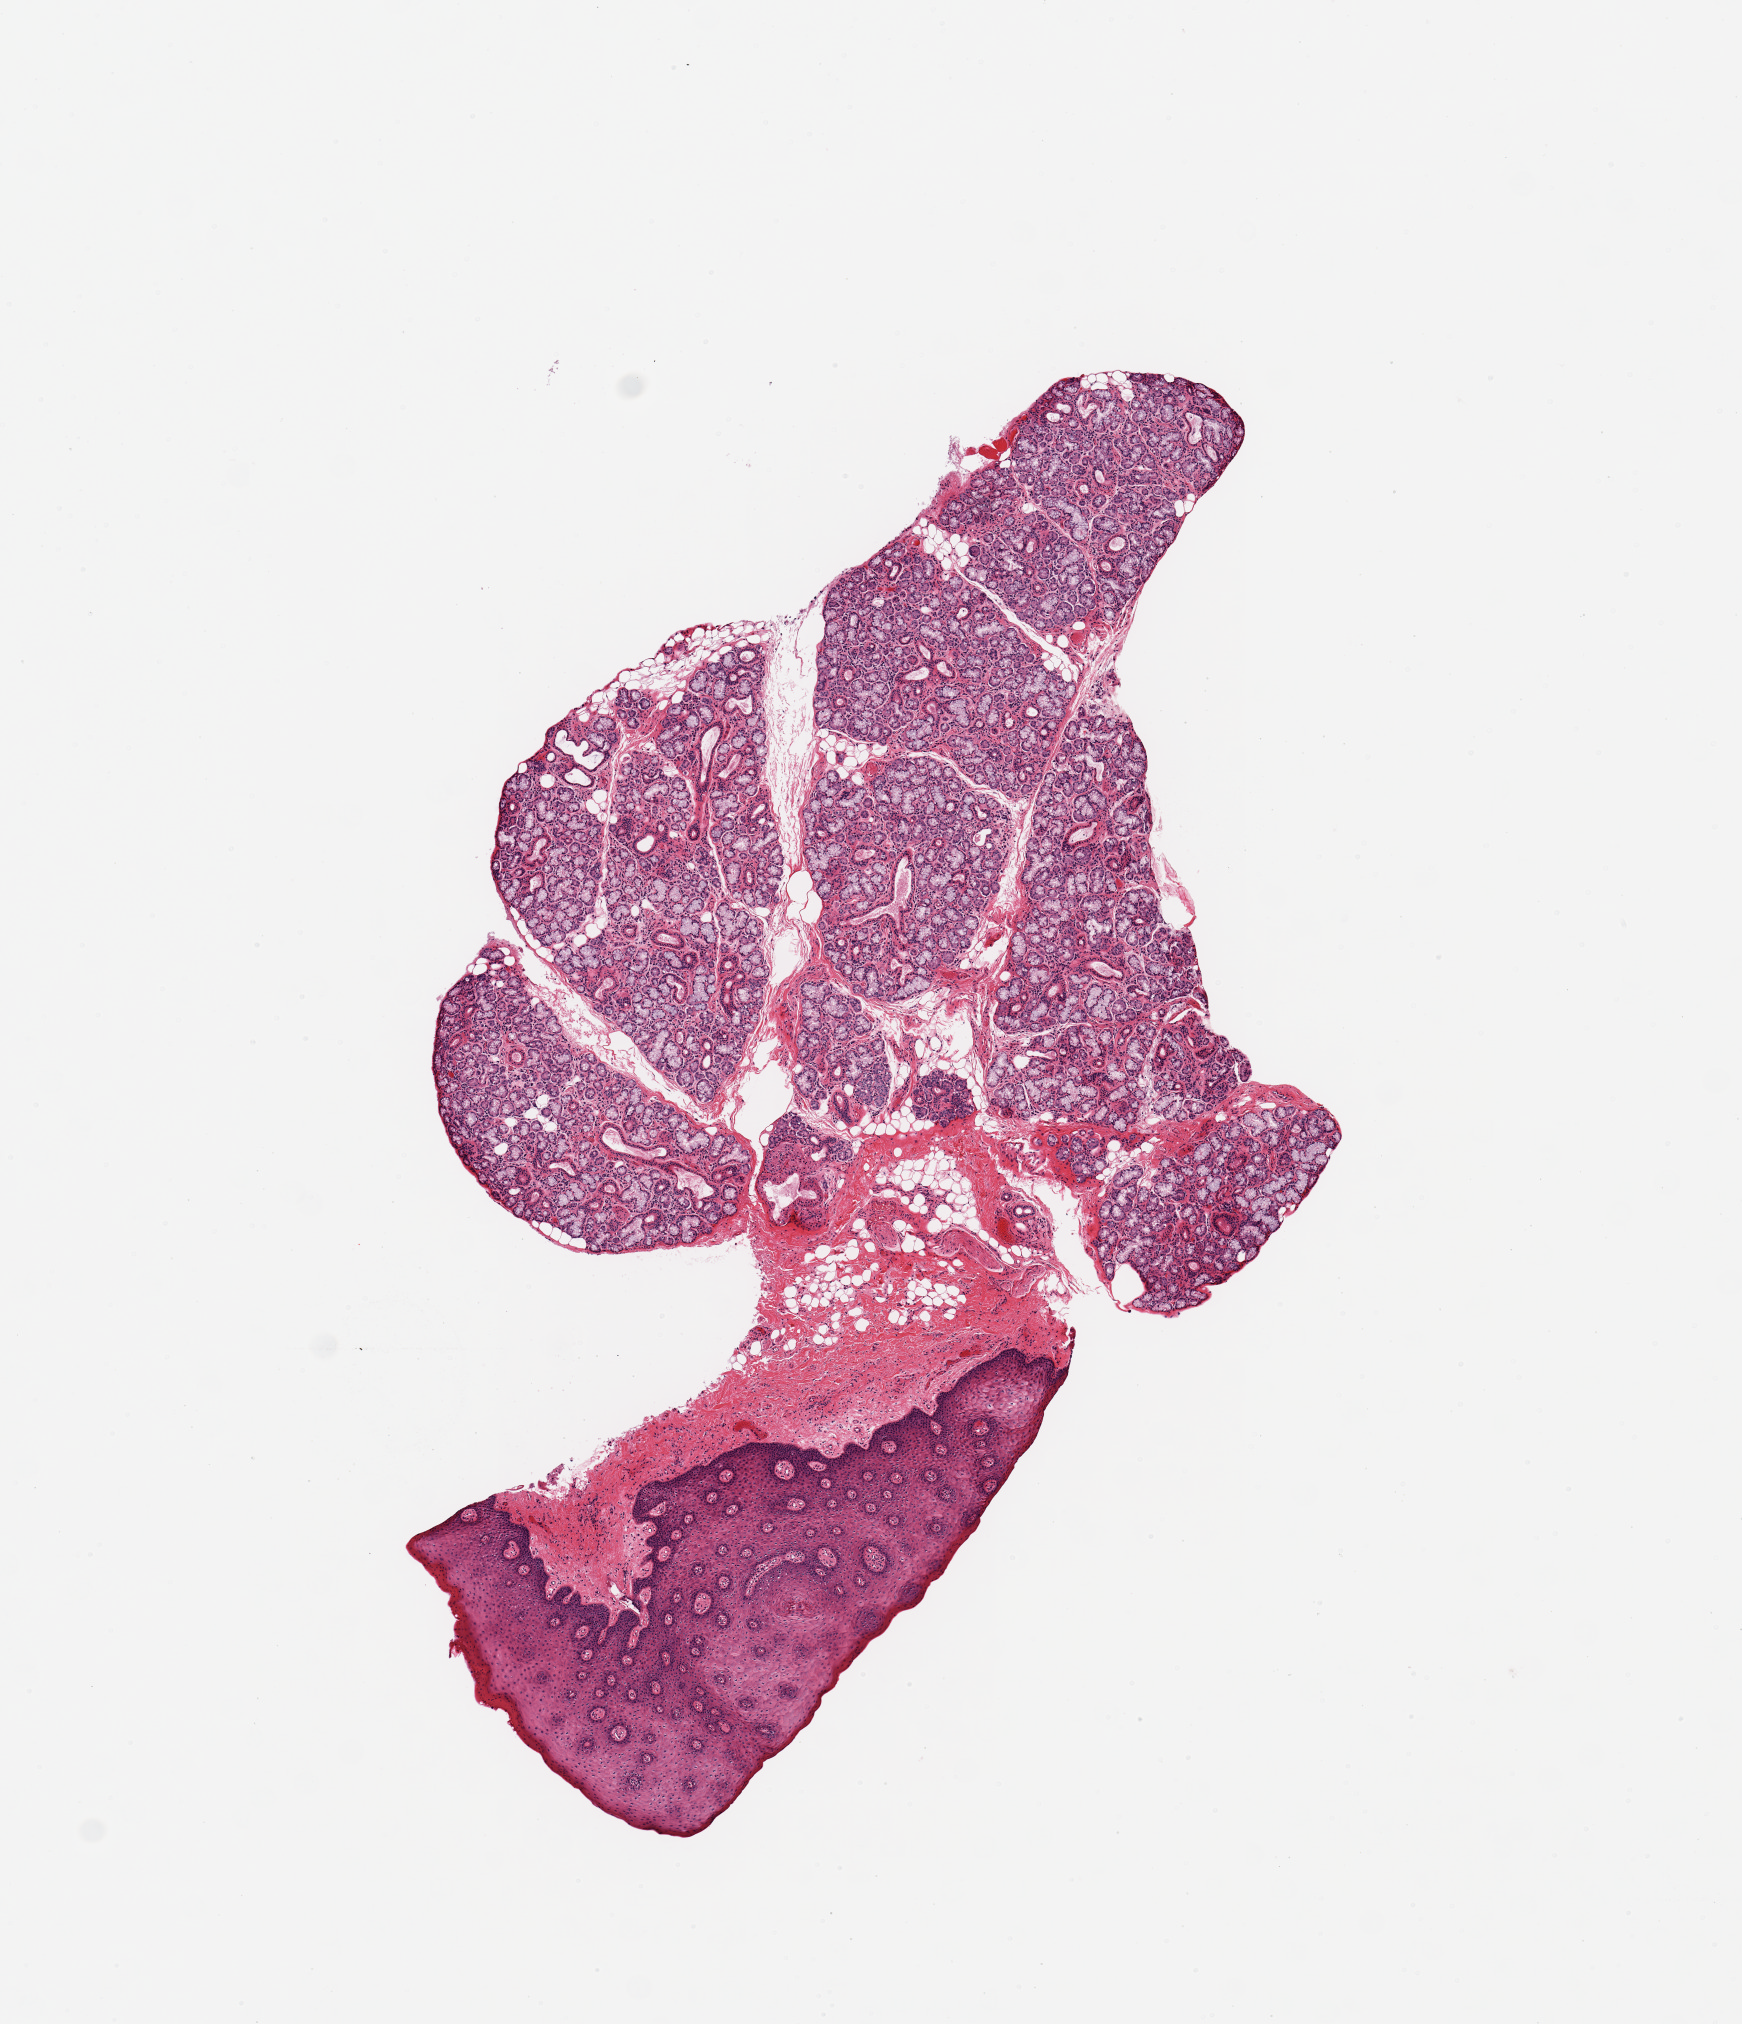
Digitized H&E-stained section — low-resolution overview of the scanned area, about 6.9 x 8.0 mm, PAXgene-fixed paraffin-embedded (PFPE) section, sampled site (target tissue): minor salivary gland, tissue donor sample.
Pathologist's review note for this sample: 1 piece; well preserved, 60% salivary gland elements, 40% lip/fat.